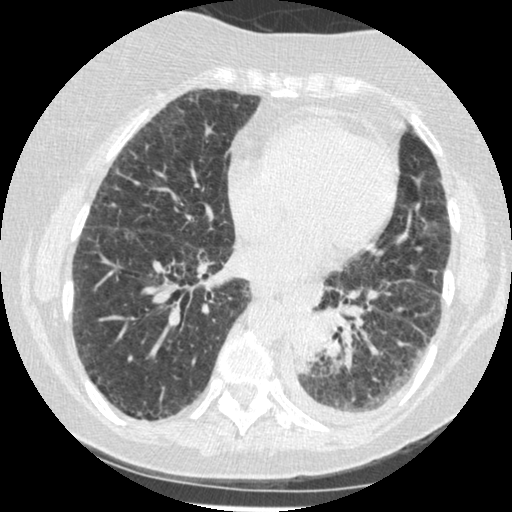
Chest CT (low-dose screening protocol), one axial image; third screening round (two years after baseline); lung window (W 1500 / L -600 HU); standard (soft-tissue) reconstruction kernel (STANDARD); 120 kVp; slice 256 of 341 in the series; 512 × 512 image matrix, field of view 310 × 310 mm. Female participant, aged 60 years at enrolment.
Expert-annotated lung lesion, bounding box [x1, y1, x2, y2] px = [278, 302, 343, 377]. Reader record for this screening exam (exam-level; its link to the box is not recorded): non-calcified nodule or mass ≥4 mm, left lower lobe, 54 × 38 mm, smooth margins, soft tissue attenuation, pre-existing on the prior screen: yes; interval growth: yes. Official screen result: positive, other. Lung cancer was diagnosed 15 days after this screen: small cell carcinoma, NOS, left lower lobe, undifferentiated (G4), stage IV (AJCC 6th edition), 69 mm at pathology.